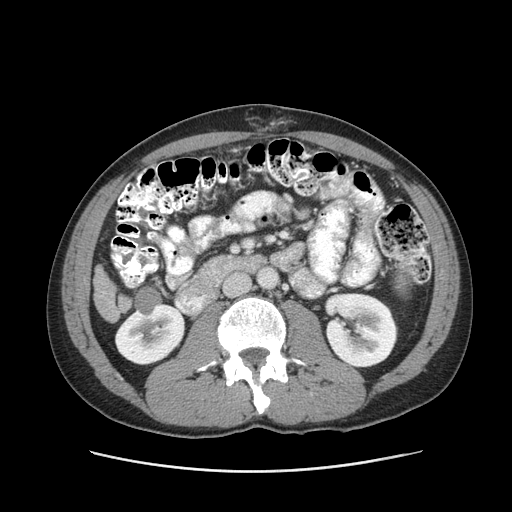
Contrast-enhanced abdominal CT (liver protocol), one axial slice; slice 26 of 93 in the series (ordered by position); 120 kVp; soft-tissue window (W 400 / L 40 HU); 2.5 mm slice thickness; 512 × 512 image matrix. From the clinical record (not read from this slice): diagnosis: hepatocellular carcinoma (patient treated with transarterial chemoembolisation; whether this scan precedes or follows treatment is not stated here); TNM stage (as recorded): Stage-II; Child-Pugh class: A; tumour size: 1 cm.
Structures marked on this image (semi-automatic segmentation, software-assisted and operator-edited):
- liver parenchyma outside the tumour (the mass and vessels are separate outlines, so this box may not span the whole liver): bounding box (x1, y1, x2, y2) in pixels: (94, 265, 116, 320)